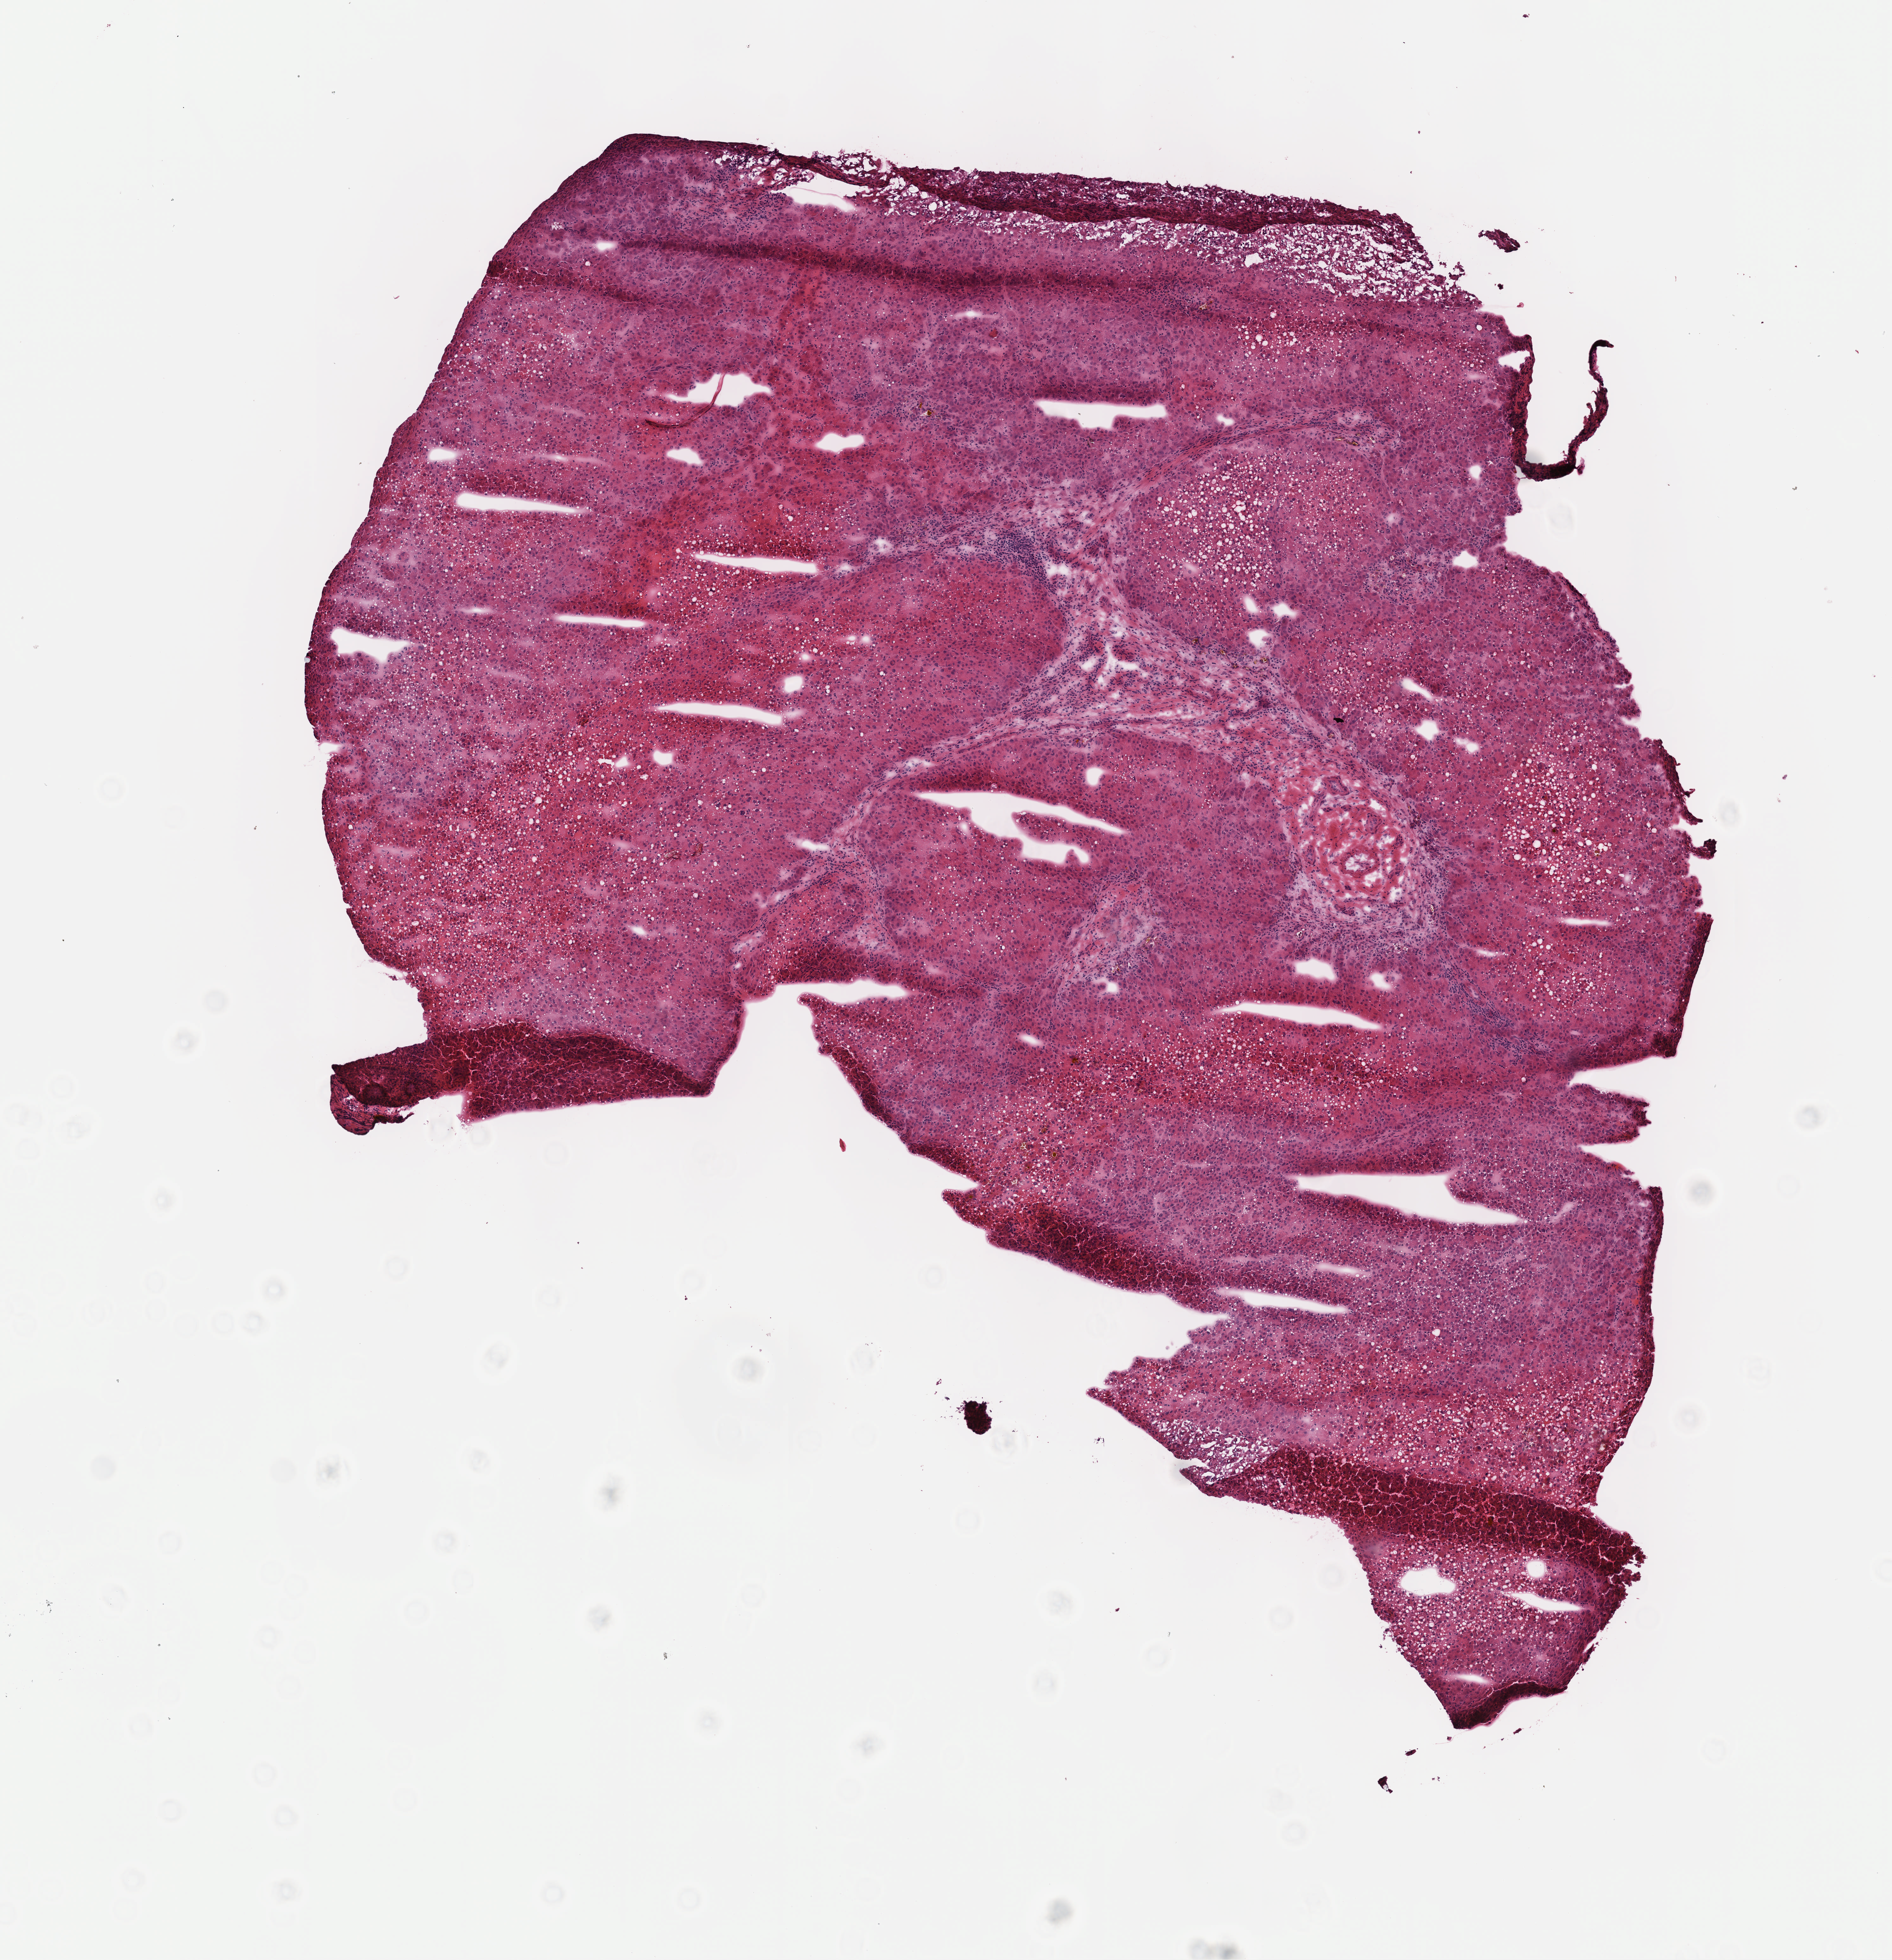
Digitized H&E-stained tissue section (whole slide) — low-resolution overview of the scanned area, about 6.0 x 6.3 mm; frozen section from the top of the tissue portion; primary tumour sample from the liver. Male patient; age at initial diagnosis 72 years. Histologic grade: G2 (moderately differentiated). Slide review estimates, as recorded: tumour cells 100%, tumour nuclei 75%, normal cells 0%, stromal cells 0%, necrosis 0%. Infiltration values recorded for this section: lymphocyte infiltration 4%, monocyte infiltration 0%, neutrophil infiltration 0%.
* AJCC pathologic stage: I (7th edition)
* histologic diagnosis: Hepatocellular carcinoma, NOS